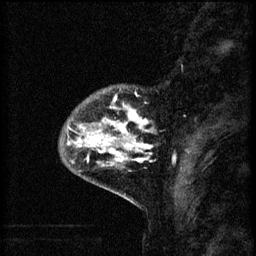
Breast MRI (dynamic contrast-enhanced), one sagittal slice. Slice 13 of 60 in the series (ordered by position). 3 images stored at this slice position (order not interpretable as contrast timing). 1.5 T. TE 4.2 ms, TR 8.2 ms. 2 mm slice thickness. 256 × 256 image matrix, field of view 180 × 180 mm. Female patient, age 41 years.
Outlined on this slice (semi-automatically segmented with operator editing):
- analysis volume of interest (the breast-tissue region the enhancement analysis was run in; not a lesion): bounding box [x1, y1, x2, y2] px = [60, 86, 155, 175]
- tumour enhancement mask (voxels above the 70 % enhancement threshold inside the analysis volume of interest): [67, 106, 153, 167]